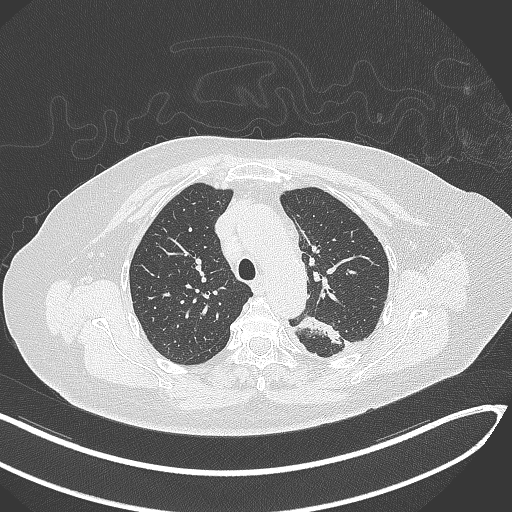
Chest CT, one axial slice; slice 231 of 270 in the series (ordered by position); reconstruction kernel B70f; lung window (W 1500 / L -600 HU); 1 mm slice thickness; 512 × 512 image matrix, field of view 400 × 400 mm. Female patient, age 76 years. From the clinical record (not read from this slice): clinical TNM (as recorded): T1c N0 M0.
Outlined on this slice (bounding box drawn by a radiologist):
- lung tumour (recorded histology: adenocarcinoma): bounding box <296,314,344,345> (left, top, right, bottom; pixels)